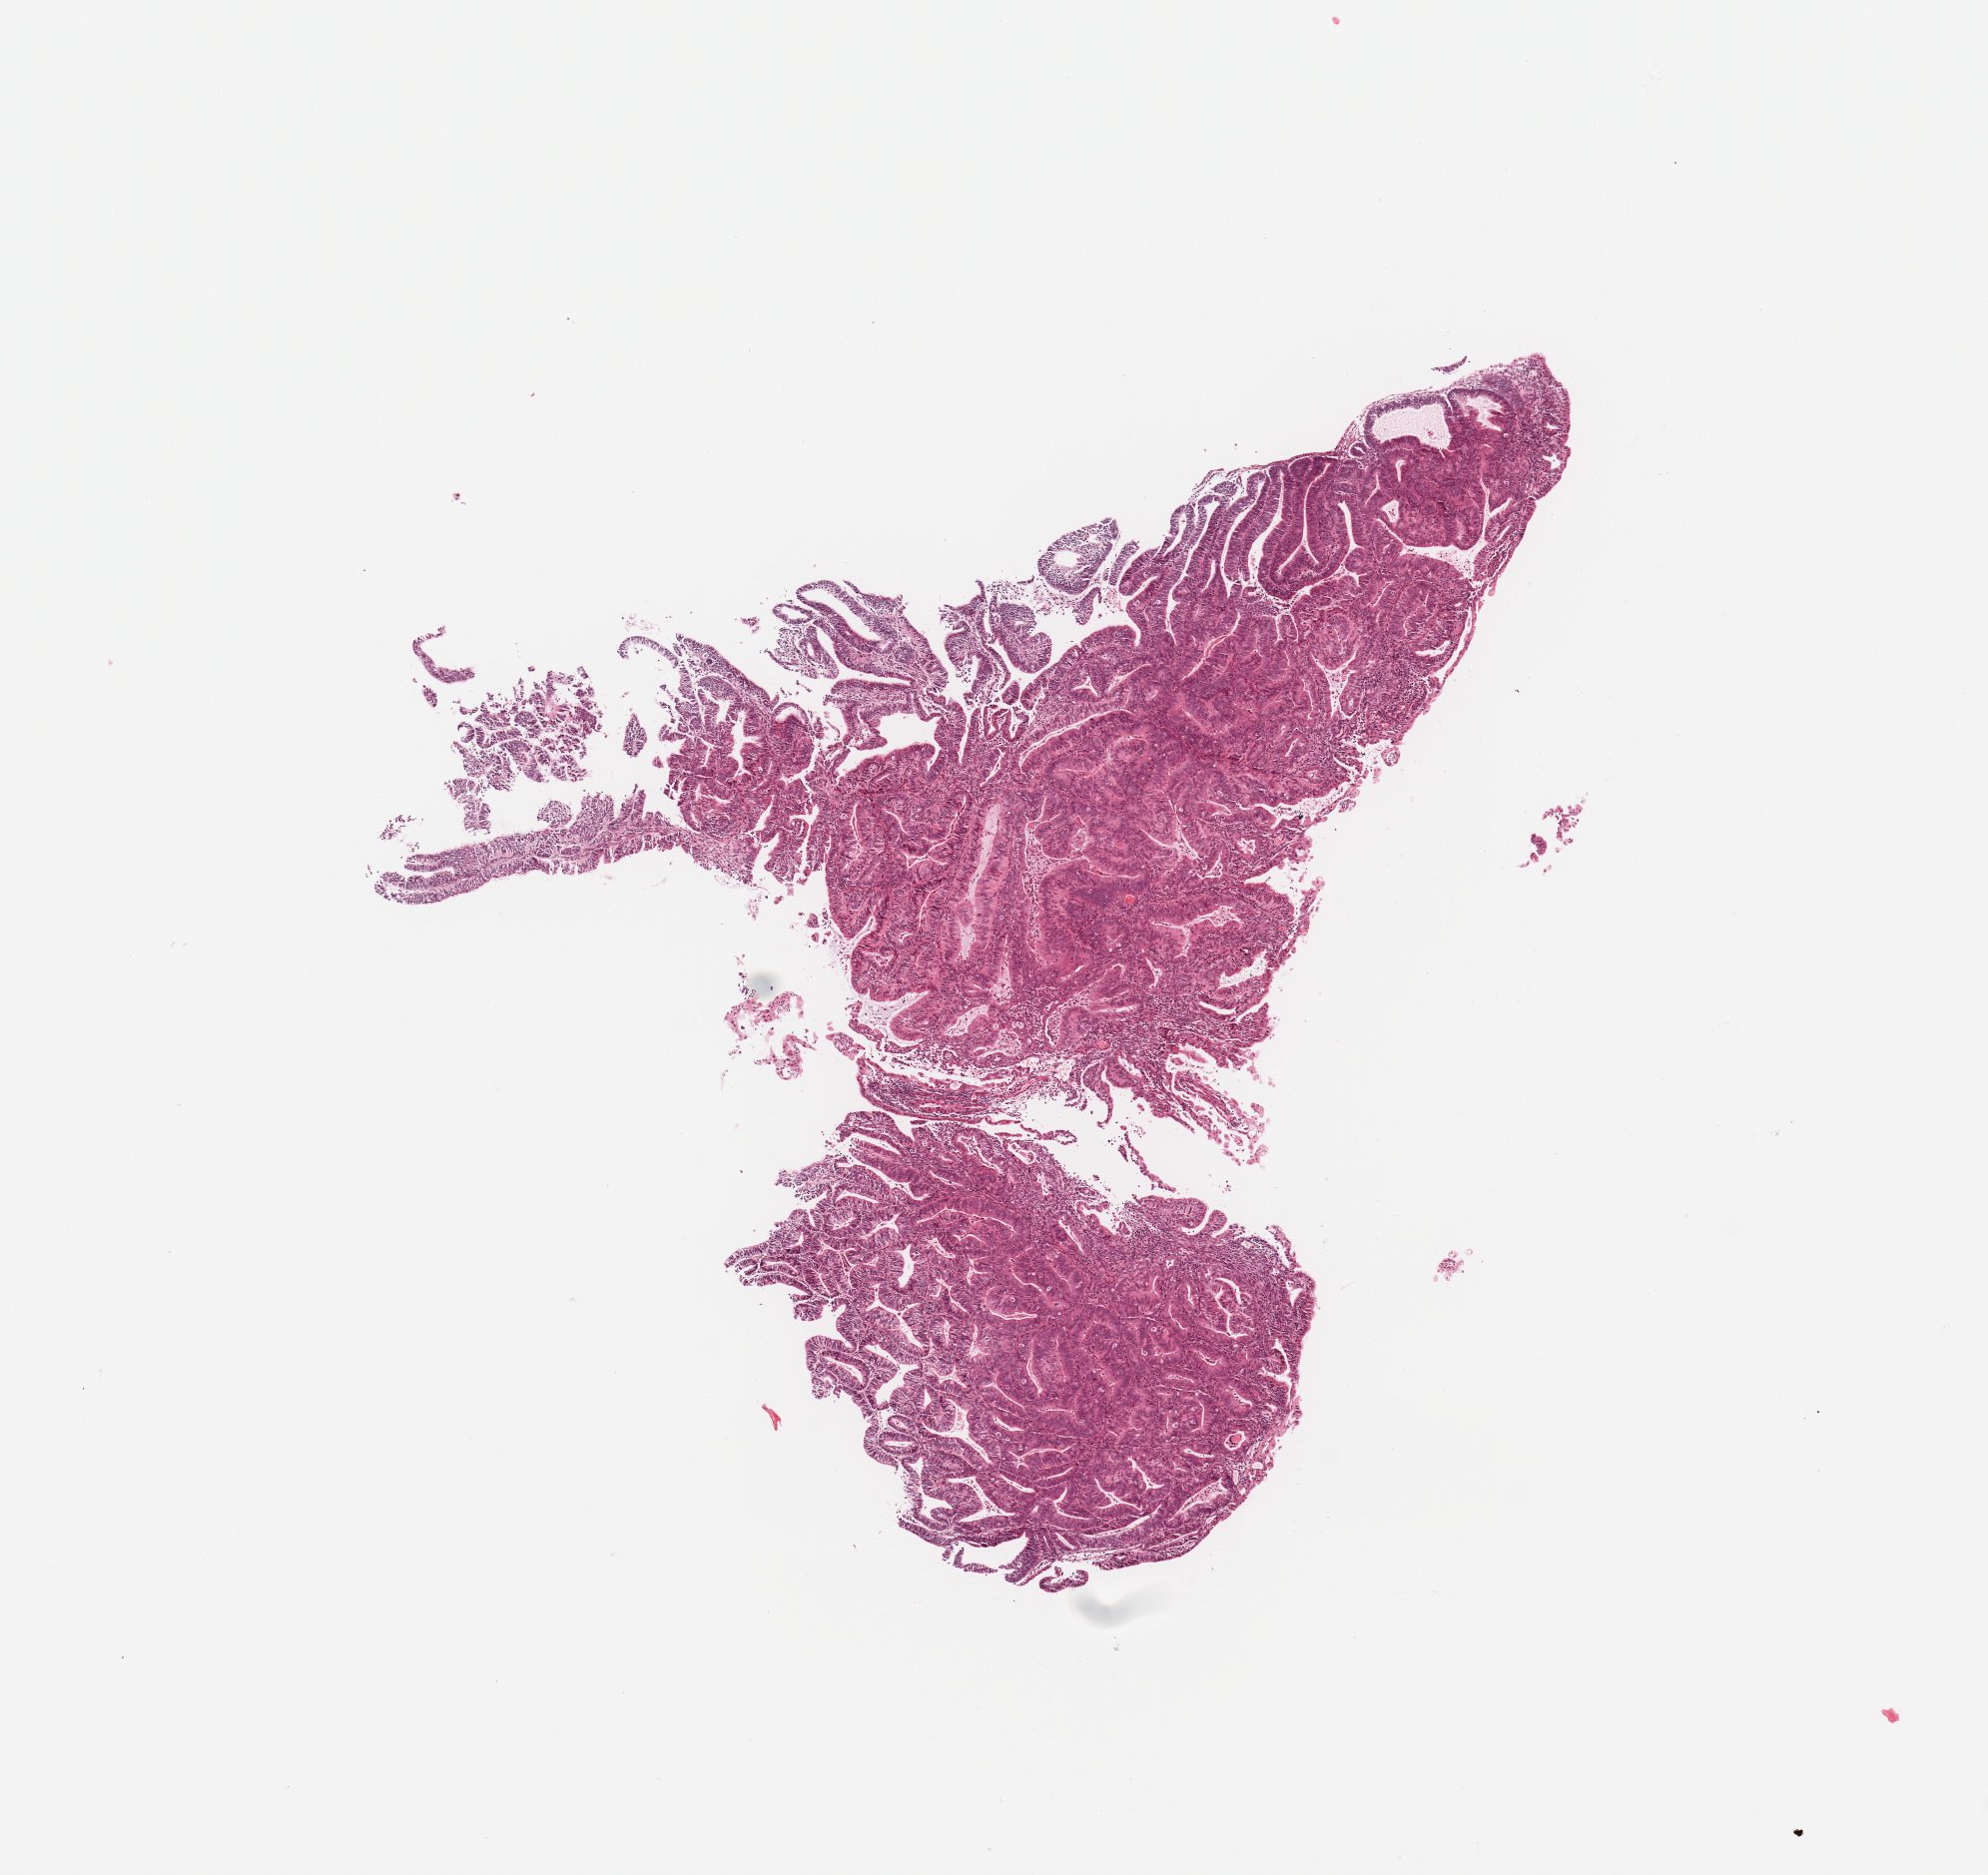
Digitized H&E tissue section (whole slide) — shown as a low-resolution overview of the whole scanned area (about 7.9 x 7.4 mm); tumour tissue sample, uterus. Patient: female, age 59 years. Histologic grade: G1 (well differentiated).
AJCC pathologic stage: IA. Diagnosis: Endometrioid adenocarcinoma, NOS.